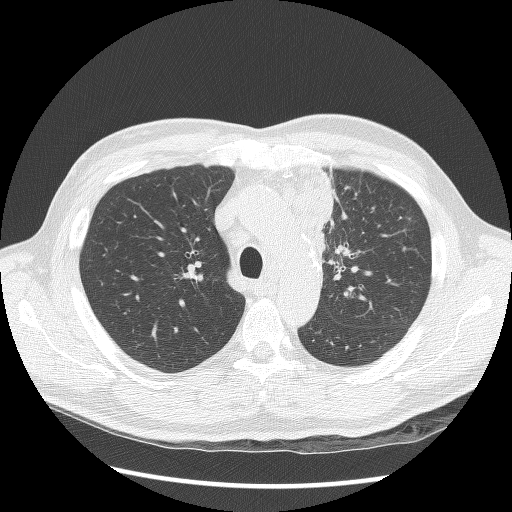
Low-dose screening chest CT, axial slice, second annual screen, lung window (W 1500 / L -600 HU), 2.5 mm slice thickness, lung (sharp) reconstruction kernel (BONE), 120 kVp. Male participant, aged 64 years at enrolment.
Lesion marked by an expert reader, bounding box [x1, y1, x2, y2] px = [296, 174, 365, 292]. Screening reader's record for this exam: no non-calcified nodule ≥4 mm recorded. Official screen result: positive, other. Later outcome: lung cancer diagnosed 24 days after this screen — small cell carcinoma, NOS, left upper lobe, stage IV (AJCC 6th edition), 100 mm at pathology.